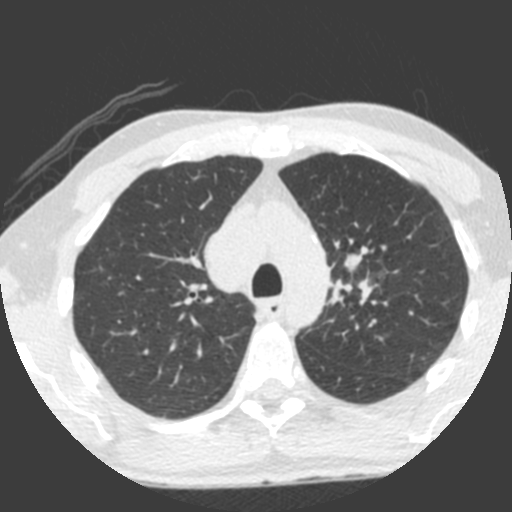
Axial slice from a low-dose chest CT screening exam. Third annual screen. Lung window (W 1500 / L -600 HU). 2 mm slice thickness. 120 kVp. Slice 157 of 212 in the series. Male participant, aged 55 years at enrolment. Current smoker at enrolment.
Lesion marked by an expert reader, bounding box [x1, y1, x2, y2] px = [308, 237, 386, 322]. Screening reader's record for this exam (one nodule recorded; not confirmed to be the boxed lesion): non-calcified nodule or mass ≥4 mm, left upper lobe, 49 × 29 mm, spiculated (stellate) margins, soft tissue attenuation, pre-existing on the prior screen: yes; interval growth: yes. Official screen result: positive, other.